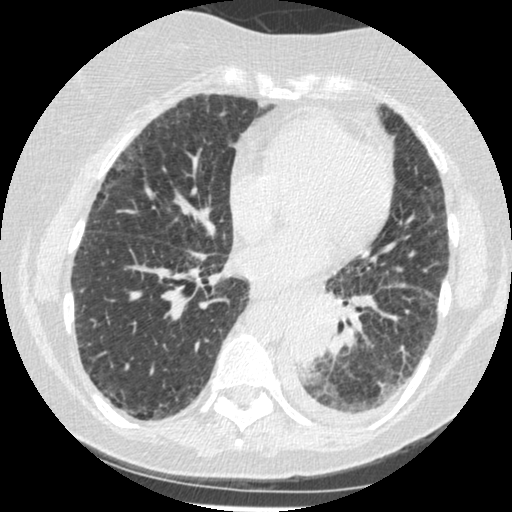
Low-dose screening chest CT, one axial slice; slice 94 of 341 in the series (ordered by position); reconstruction kernel STANDARD; lung window (W 1500 / L -600 HU); 1.25 mm slice thickness; 512 × 512 image matrix, field of view 310 × 310 mm.
Outlined on this slice (outlined manually by an expert reader):
- lesion 1 (tumor, lower lobe of left lung): box from (x=288, y=310) to (x=331, y=366) px